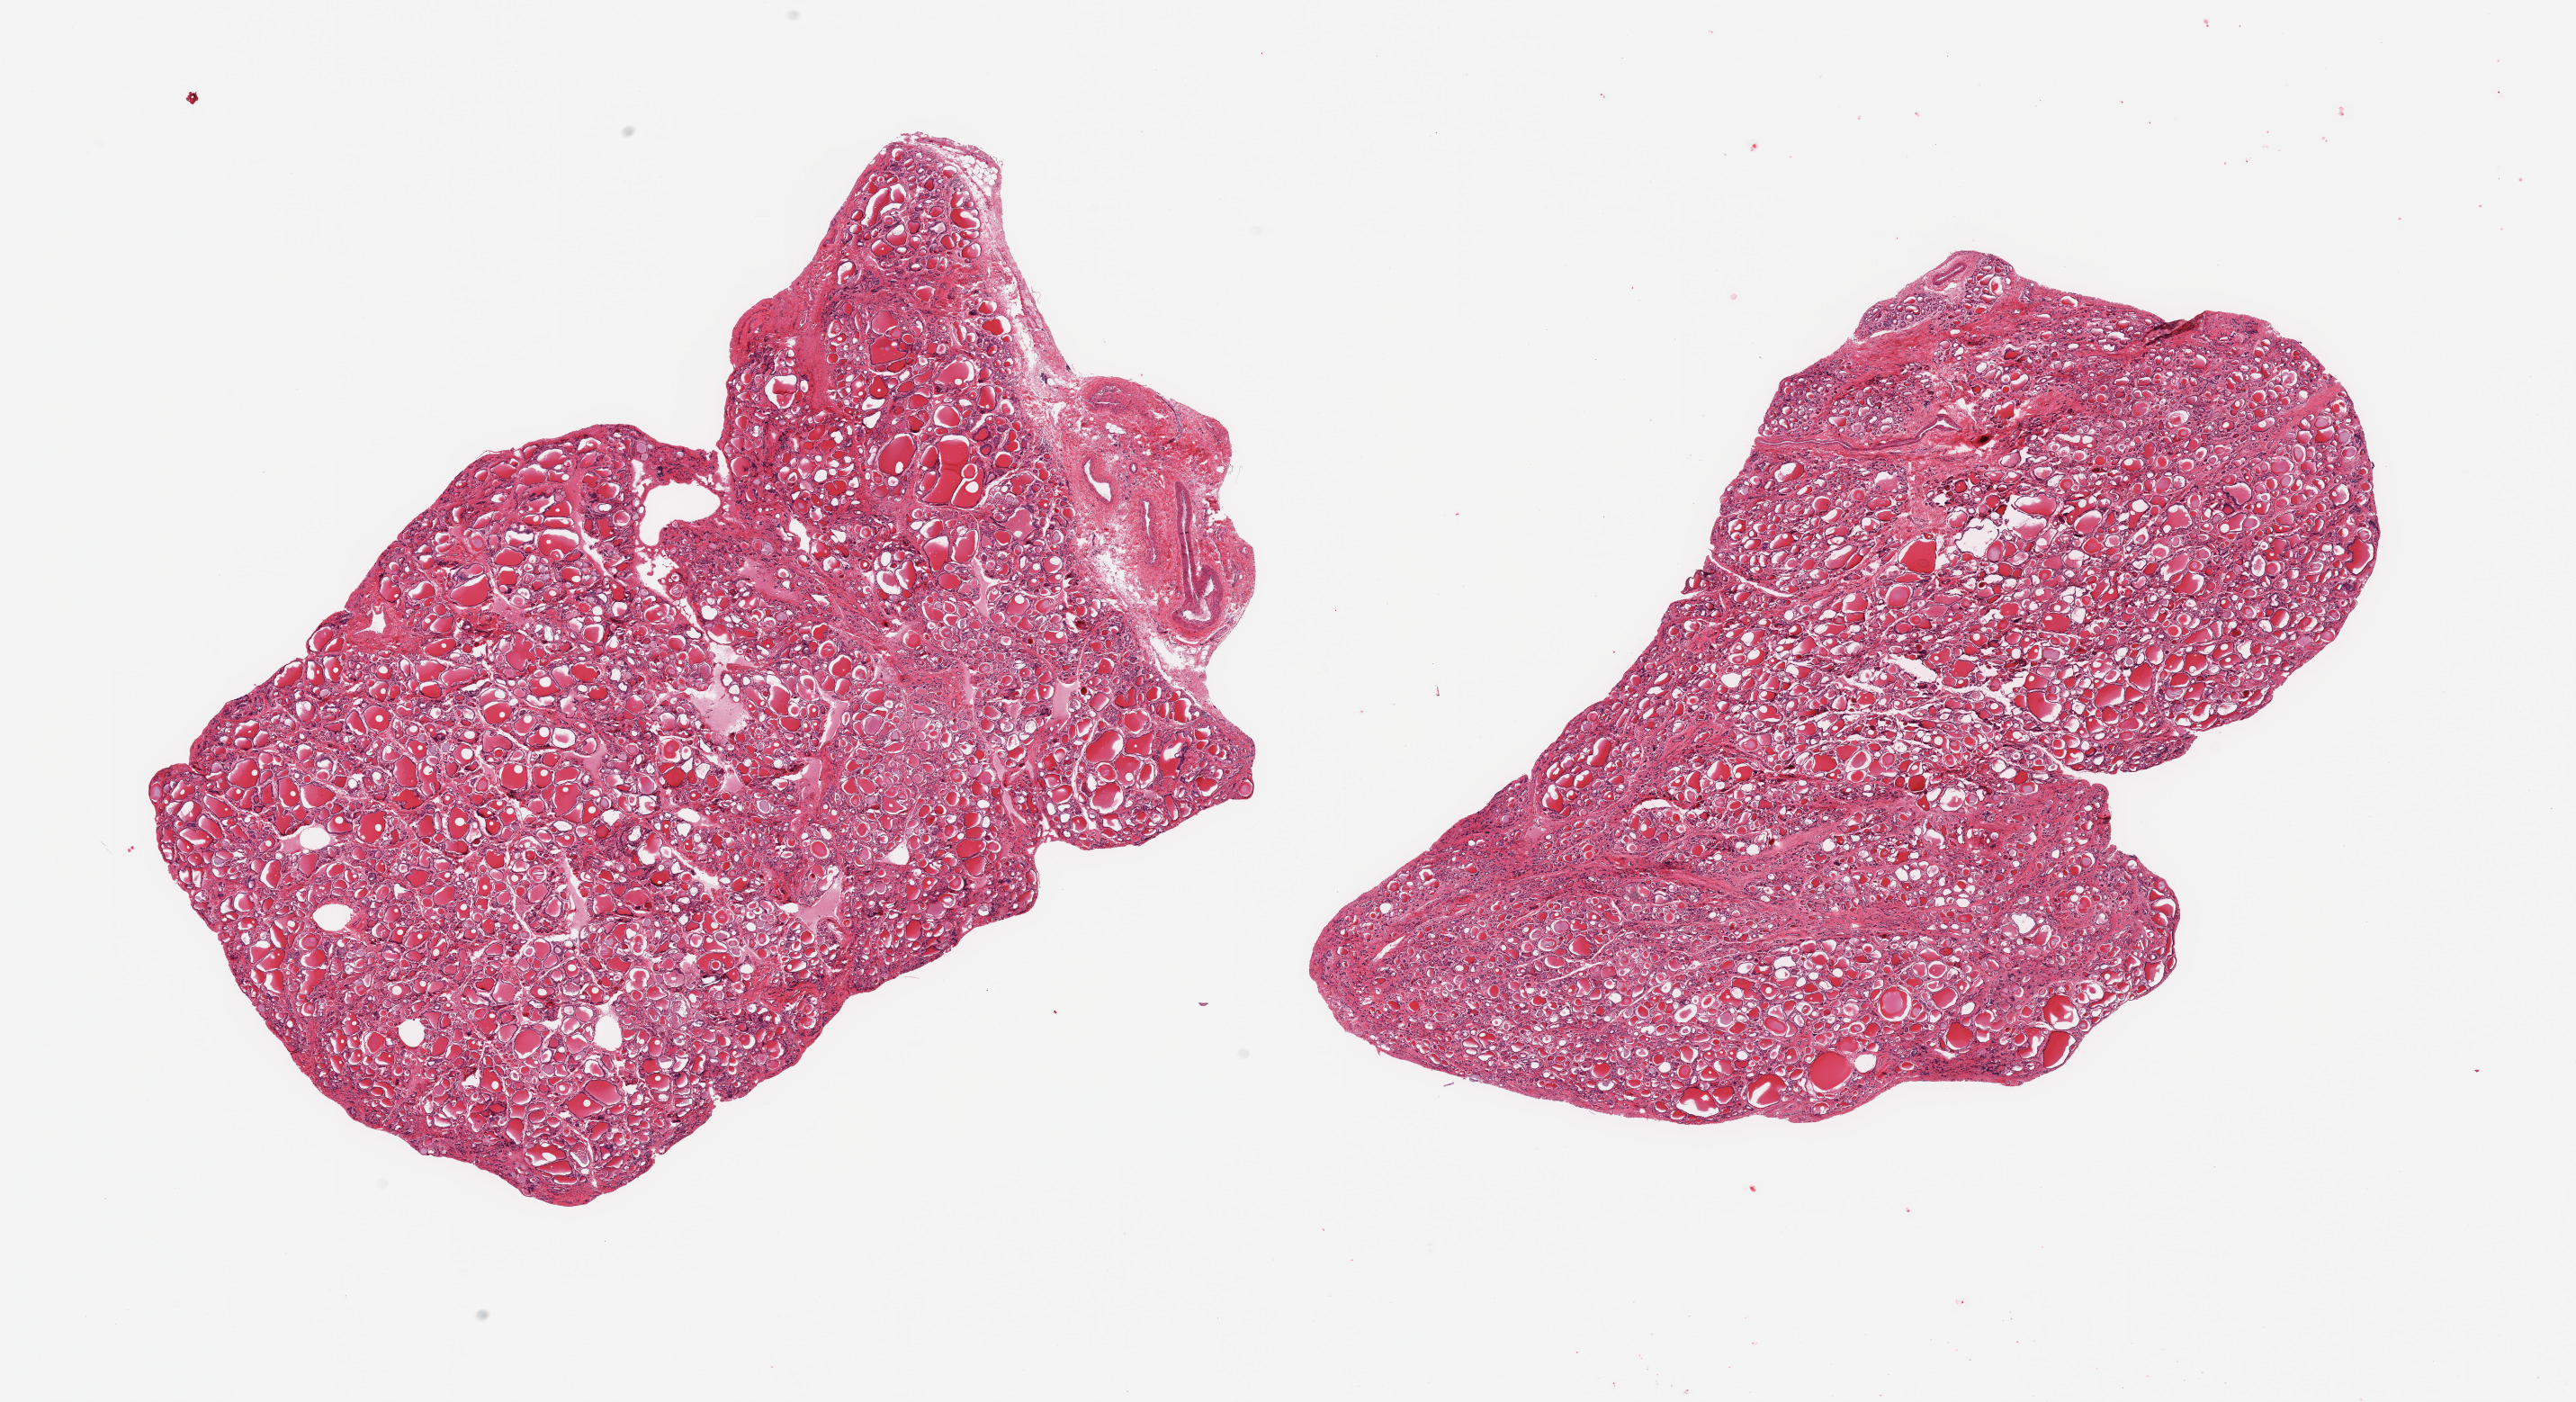
Digitized hematoxylin and eosin (H&E)-stained section — whole scanned area (about 22.6 x 12.3 mm) shown as a low-resolution overview; PAXgene-fixed paraffin-embedded (PFPE) section; target tissue: thyroid; tissue donor sample. Female donor.
- pathologist's review note for this sample: 2 pieces; 2.6x1.4mm fibrovascular area on edge of 1 piece, otherwise well dissected